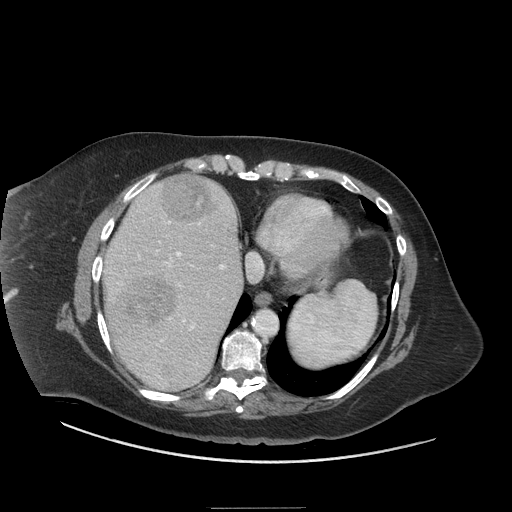
Contrast-enhanced abdominal CT (liver protocol), one axial slice; slice 56 of 81 in the series (ordered by position); reconstruction kernel STANDARD; soft-tissue window (W 400 / L 40 HU); 2.5 mm slice thickness; 512 × 512 image matrix, field of view 440 × 440 mm. From the clinical record (not read from this slice): diagnosis: hepatocellular carcinoma (patient treated with transarterial chemoembolisation; whether this scan precedes or follows treatment is not stated here); TNM stage (as recorded): Stage-II; Child-Pugh class: A; tumour differentiation: moderately differentiated.
Annotated regions visible in this slice (semi-automatically segmented with operator editing):
- liver parenchyma outside the tumour (the mass and vessels are separate outlines, so this box may not span the whole liver): bounding box [x1, y1, x2, y2] px = [102, 178, 242, 390]
- mass: [117, 172, 213, 389]
- liver vessels: [110, 204, 226, 379]